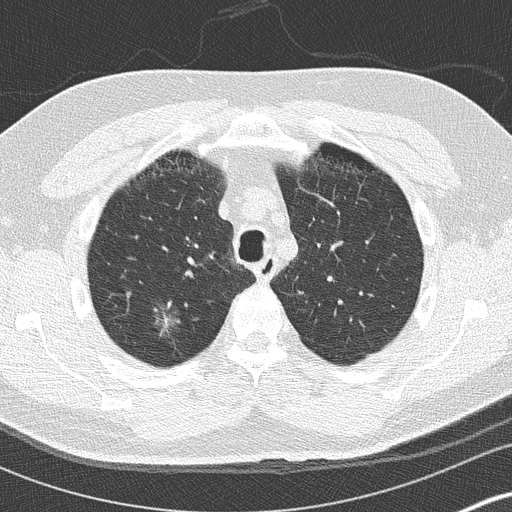
Chest CT (low-dose screening protocol), one axial image, baseline annual screen, lung window (W 1500 / L -600 HU), 2 mm slice thickness, slice 34 of 136 in the series. Male, age 59 years at enrolment. Current smoker at enrolment.
Expert-annotated lung lesion, box from (x=144, y=291) to (x=196, y=343) px. Screening reader's record for this exam (one nodule recorded; not confirmed to be the boxed lesion): non-calcified nodule or mass ≥4 mm, right upper lobe, 16 × 16 mm, ground glass attenuation. Official screen result: positive, change unspecified: nodule(s) >= 4 mm or enlarging nodule(s), mass(es), or other non-specific abnormalities suspicious for lung cancer. Lung cancer was diagnosed 456 days after this screen: bronchiolo-alveolar adenocarcinoma, NOS, right lower lobe, stage IA (AJCC 6th edition), 15 mm at pathology.